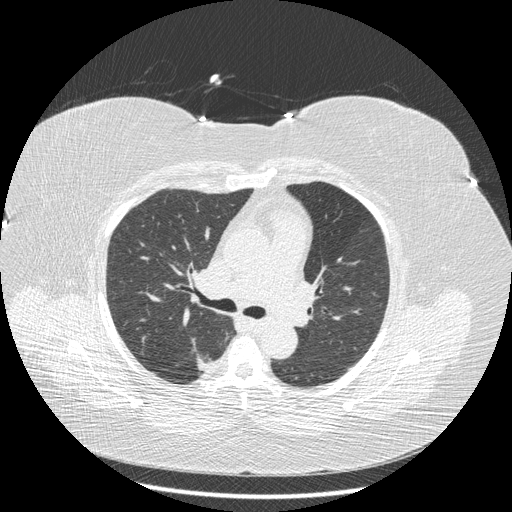
Axial slice from a low-dose chest CT screening exam. Baseline screening round. Lung window (W 1500 / L -600 HU). Slice 77 of 211 in the series. 512 × 512 image matrix. Female participant, aged 58 years at enrolment.
Expert reader's lesion annotation, bounding box (x1, y1, x2, y2) in pixels: (184, 346, 225, 383). Screening reader's record for this exam (one nodule recorded; not confirmed to be the boxed lesion): non-calcified nodule or mass ≥4 mm, right lower lobe, 15 × 10 mm, smooth margins, soft tissue attenuation. Participant outcome: lung cancer diagnosed 362 days after this screen — adenocarcinoma, NOS, right lower lobe, stage IB (AJCC 6th edition), 15 mm at pathology.